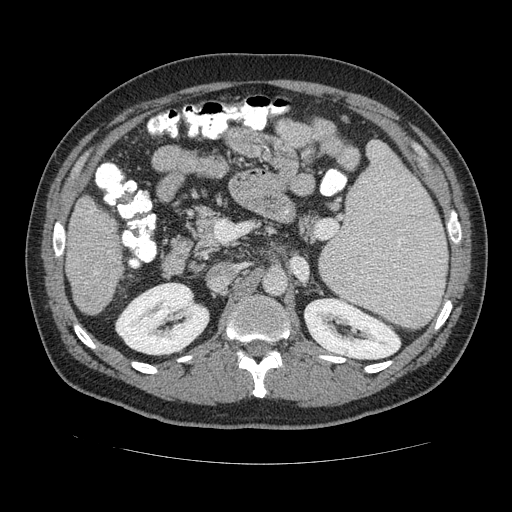
Contrast-enhanced abdominal CT (liver protocol), one axial slice. Slice 59 of 113 in the series (ordered by position). Reconstruction kernel STANDARD. 120 kVp. Soft-tissue window (W 400 / L 40 HU). 2.5 mm slice thickness. 512 × 512 image matrix. Case-level facts recorded for this patient, not image findings: diagnosis: hepatocellular carcinoma (patient treated with transarterial chemoembolisation; whether this scan precedes or follows treatment is not stated here); TNM stage (as recorded): Stage-II; Child-Pugh class: B; tumour differentiation: moderately differentiated; tumour nodularity: multinodular.
Structures marked on this image (semi-automatic segmentation, software-assisted and operator-edited):
- liver parenchyma outside the tumour (the mass and vessels are separate outlines, so this box may not span the whole liver): bounding box [x1, y1, x2, y2] px = [64, 192, 124, 316]
- liver vessels: [87, 220, 96, 273]